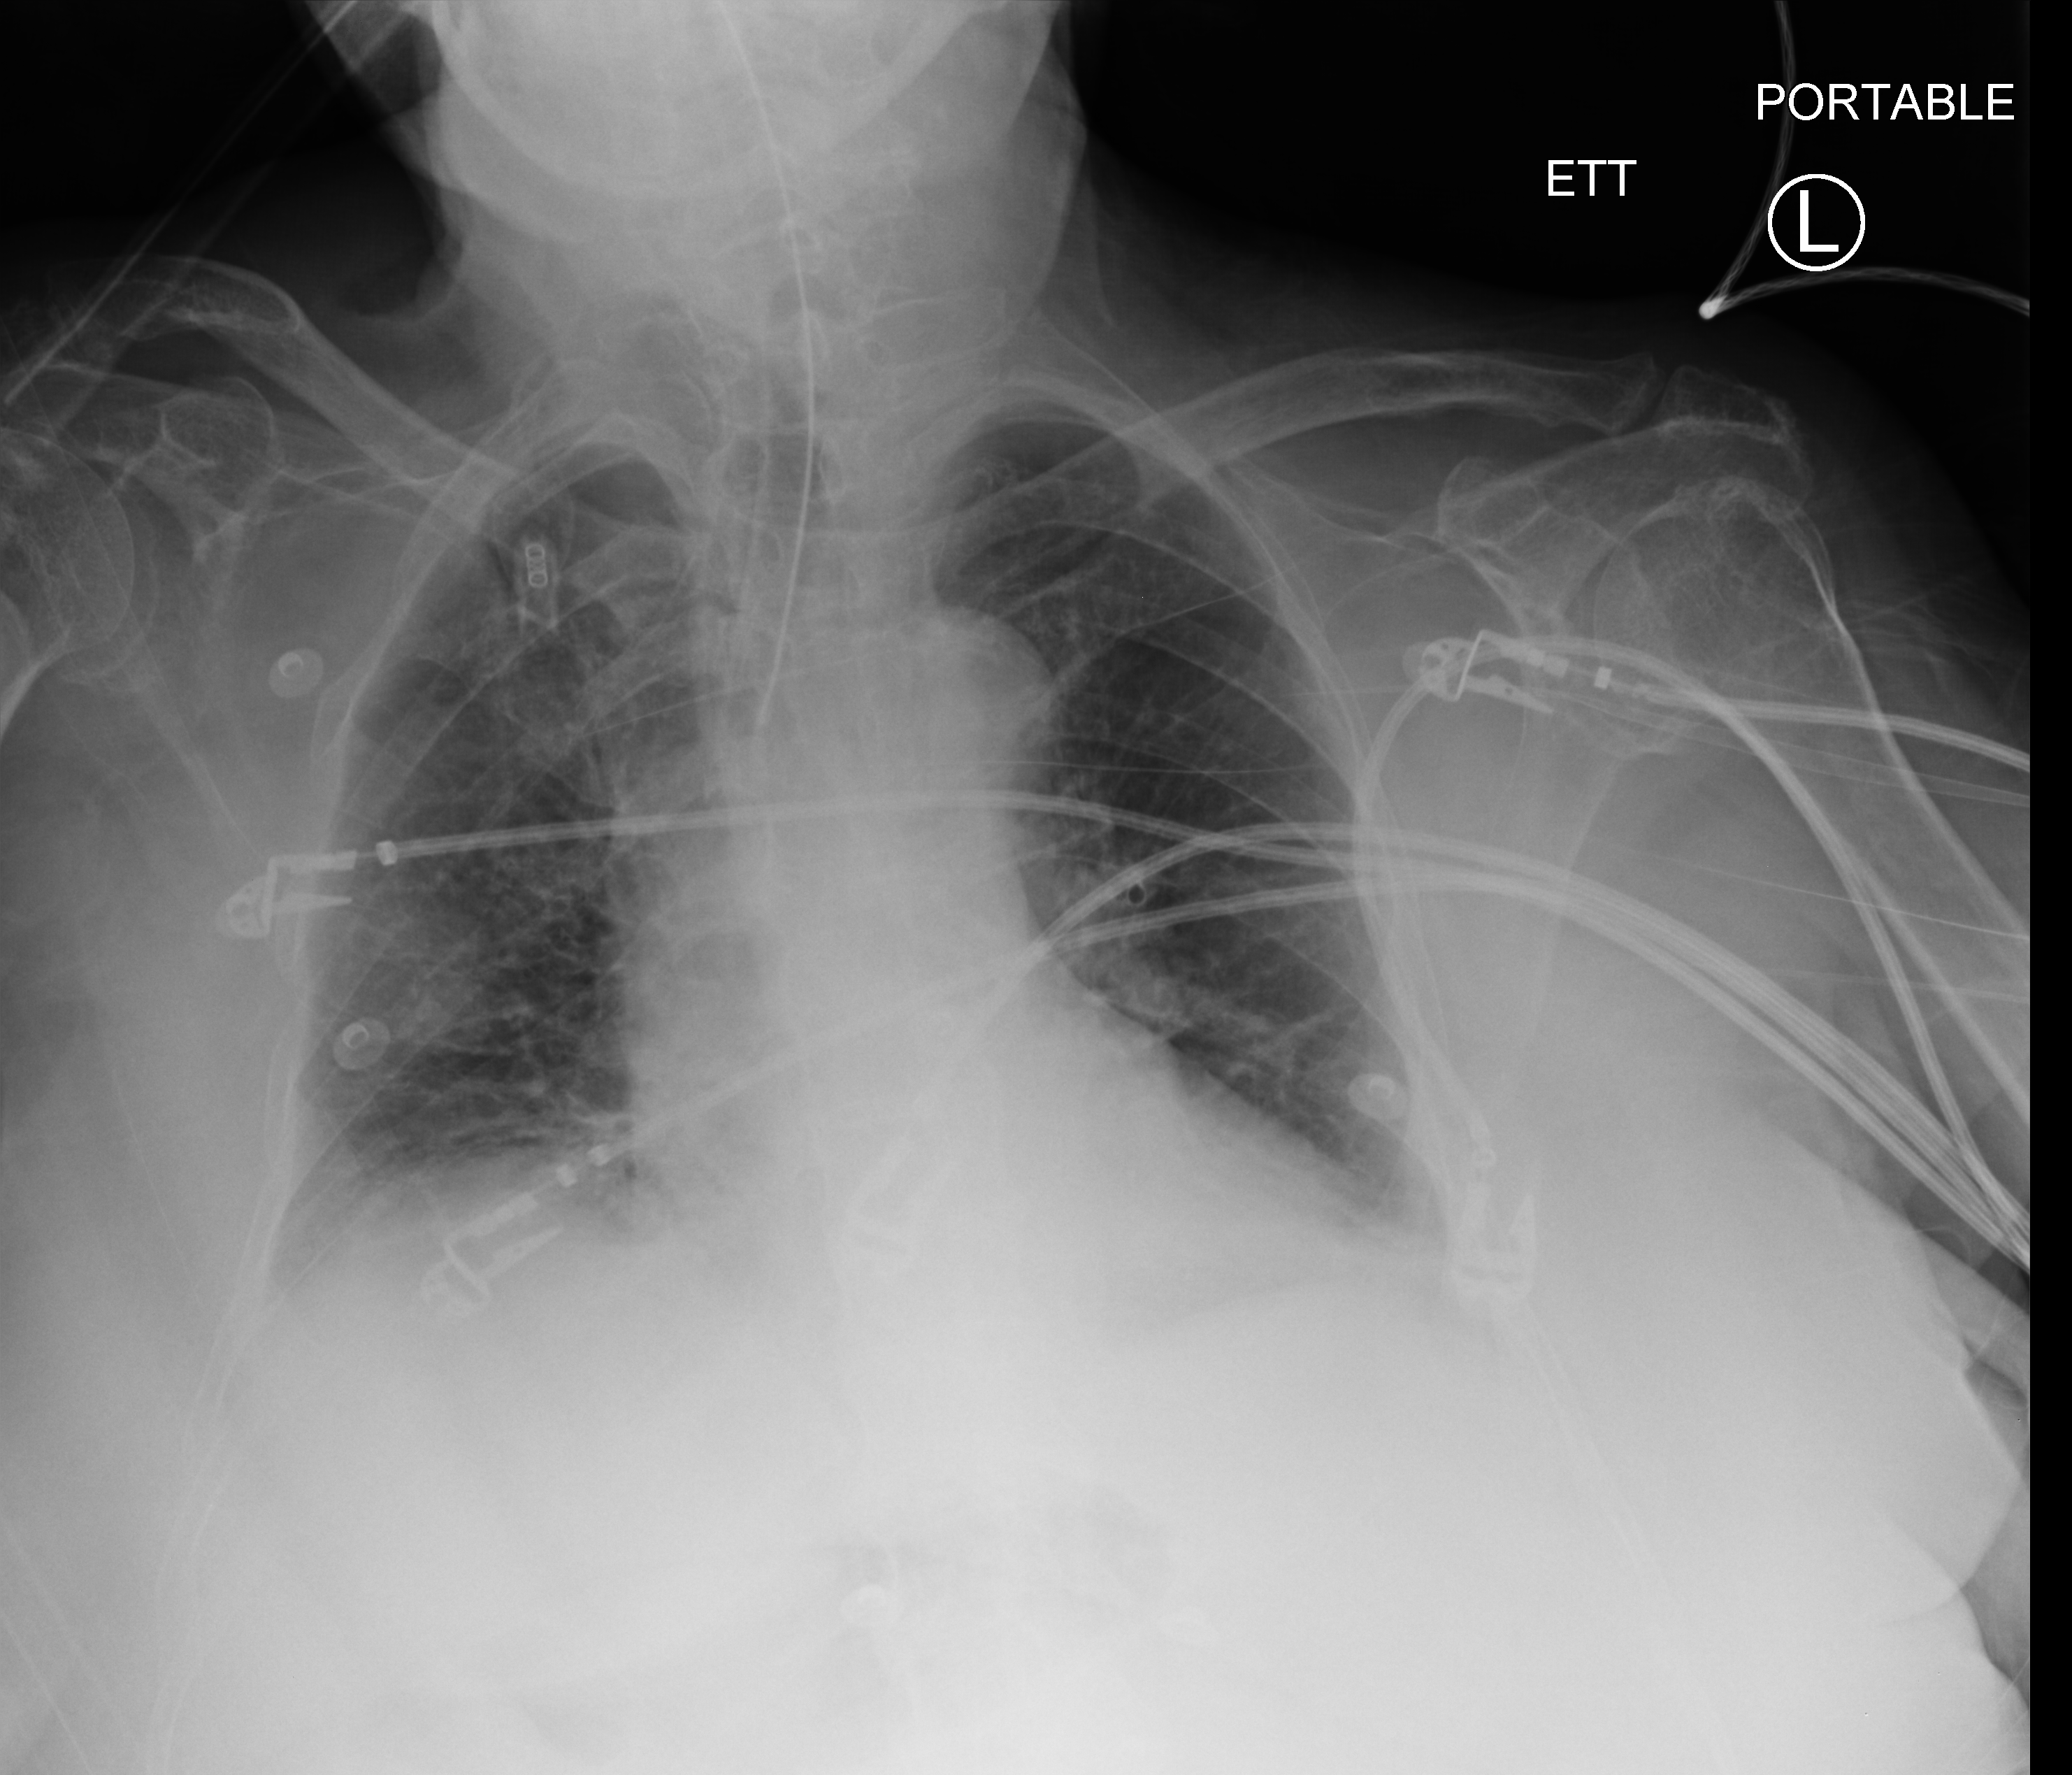
Chest X-ray (portable); anteroposterior (AP) projection. Female patient hospitalised with COVID-19, age 75–90 years.
From the hospital-stay record, not from the radiograph (when in the stay this image was taken is not recorded): admitted to intensive care during this hospital stay: yes; mechanically ventilated during this hospital stay: yes; length of hospital stay: 14 days.